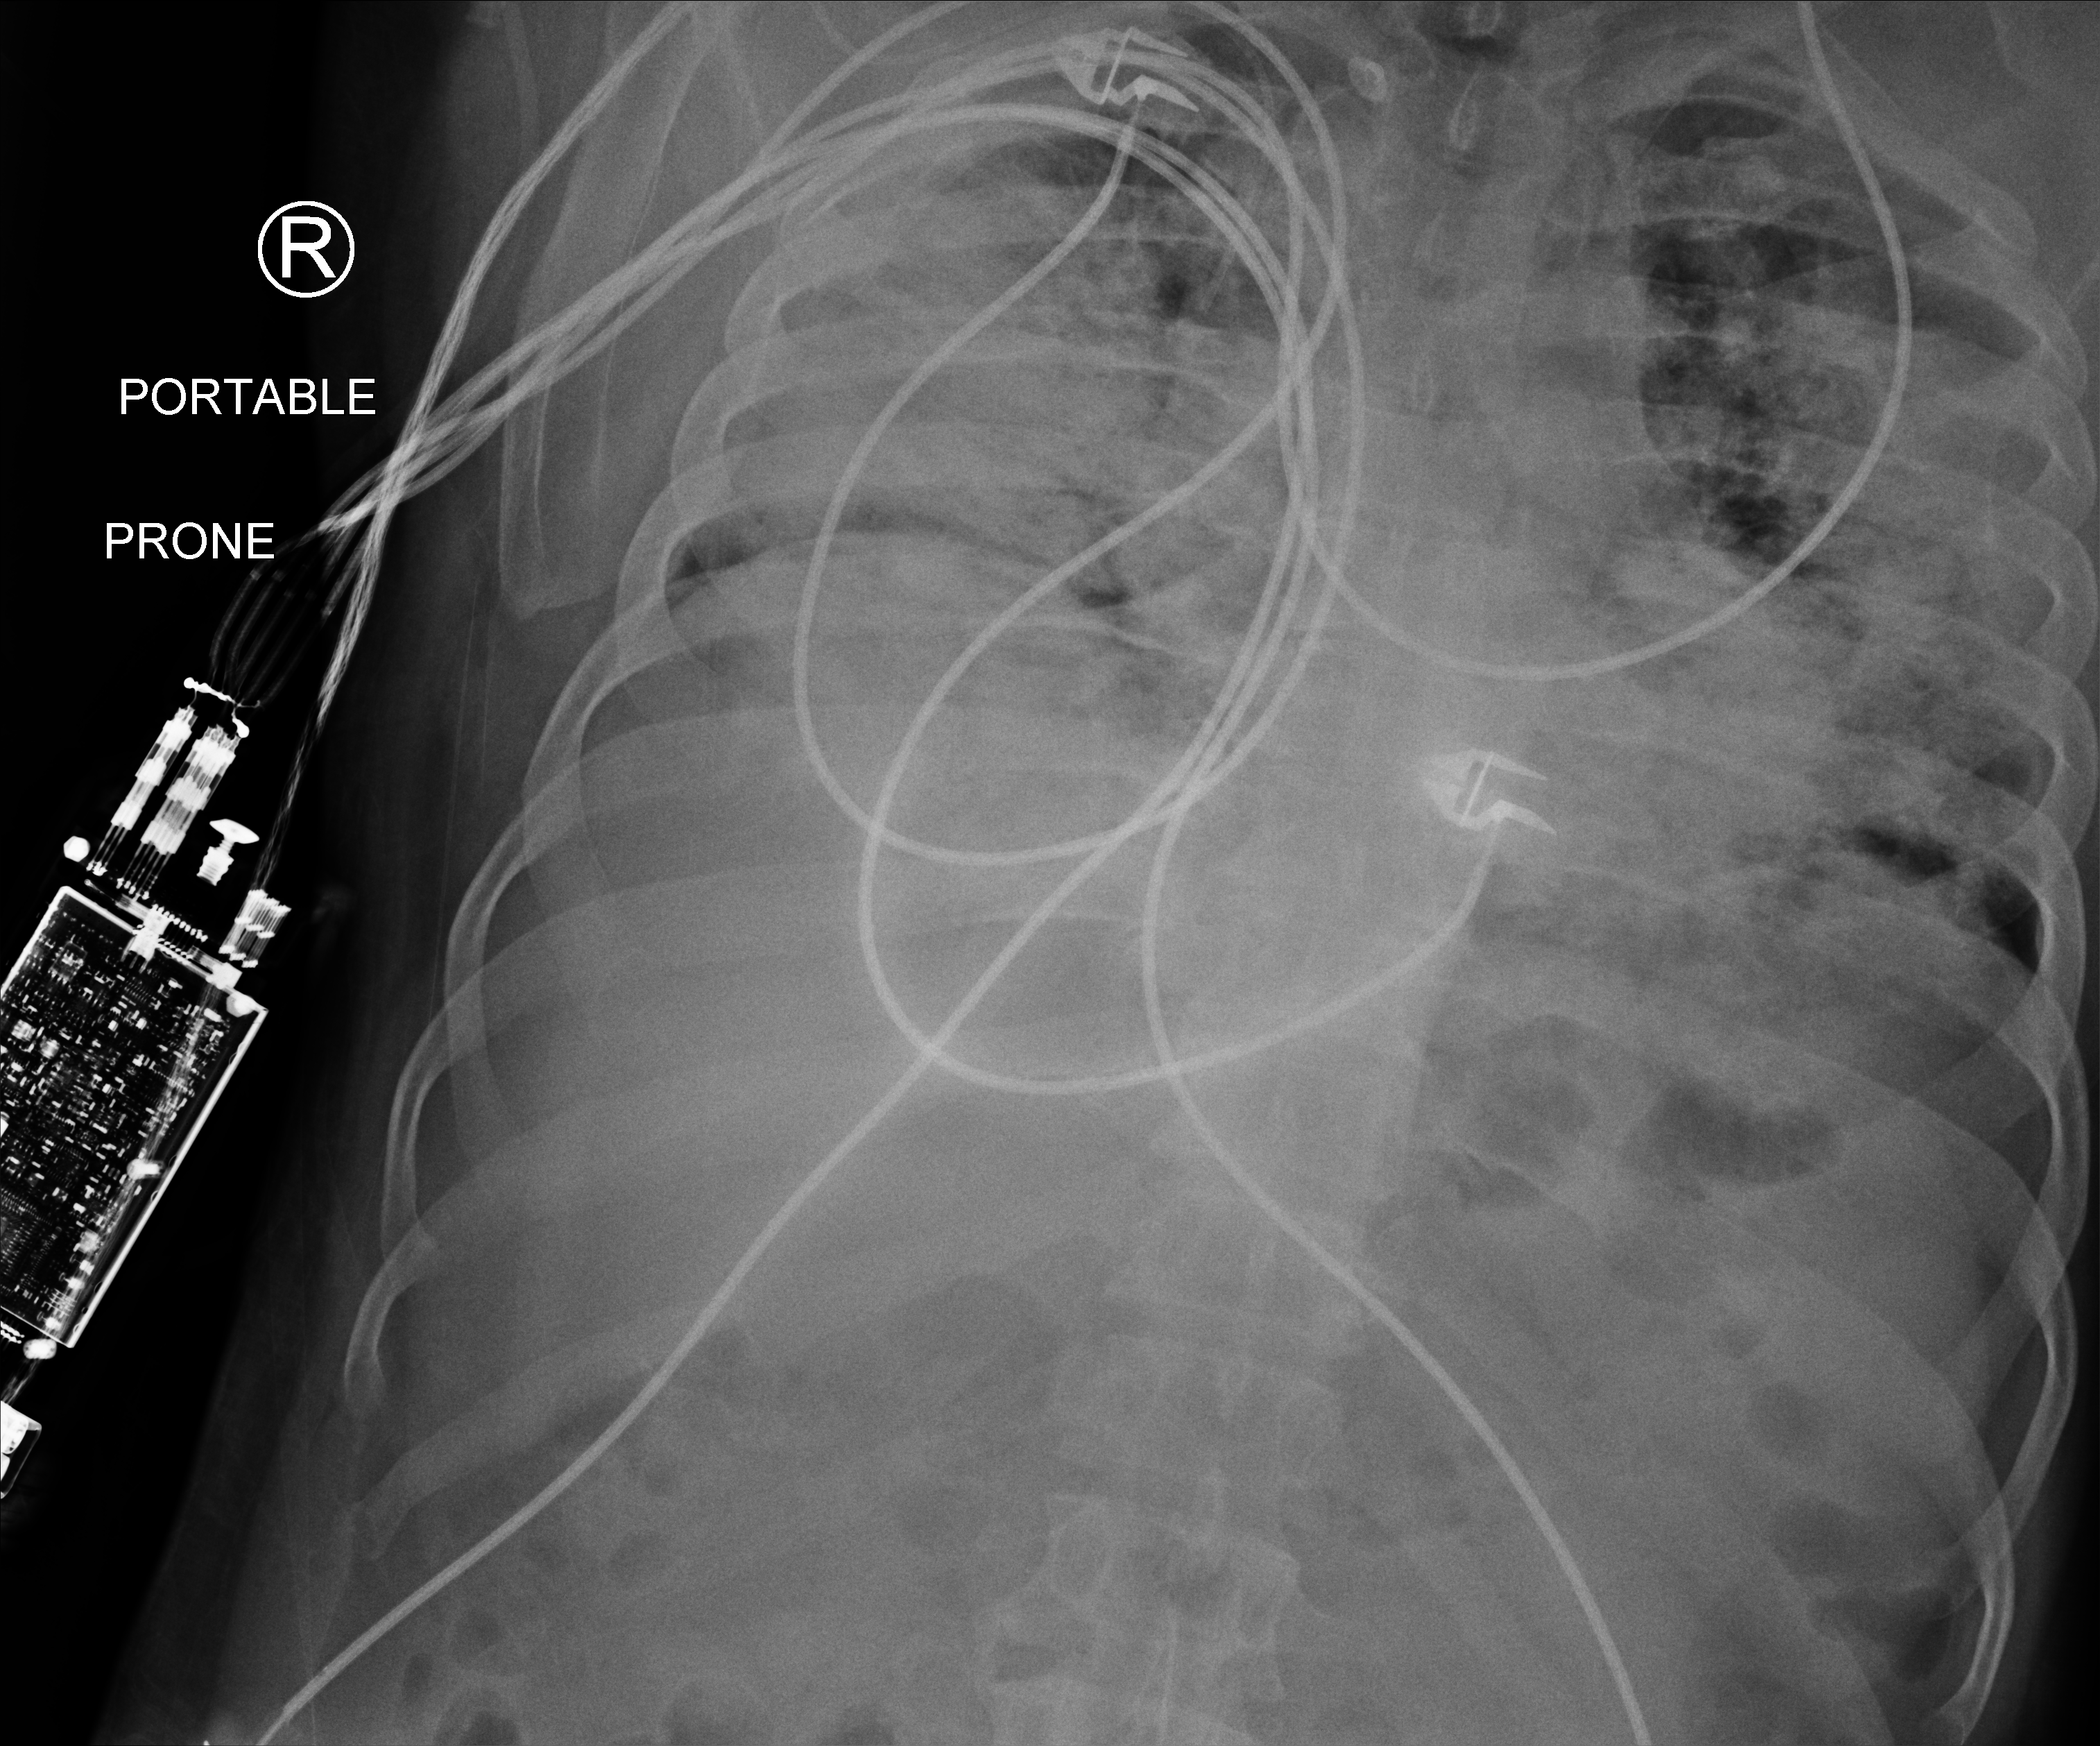
Chest X-ray (portable); posteroanterior (PA) projection. Male patient hospitalised with COVID-19, age 18–59 years.
Hospital-stay facts (about this admission, not read from this image; timing relative to this image not recorded):
- smoking status (admission record): never